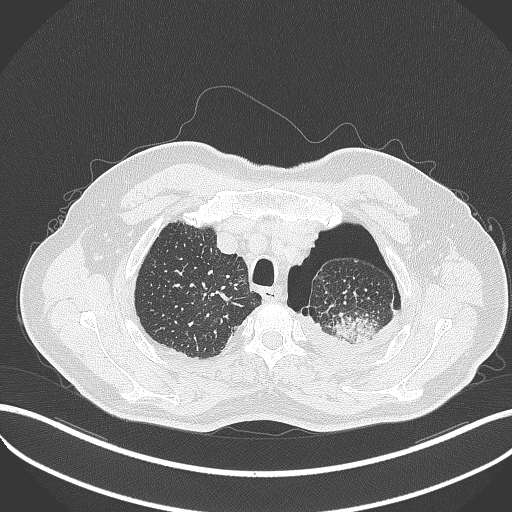
Chest CT, one axial slice; slice 420 of 464 in the series (ordered by position); lung window (W 1500 / L -600 HU); 512 × 512 image matrix. Patient: male, 76 years. From the clinical record (not read from this slice): clinical TNM (as recorded): T3 N0 M1b.
Structures marked on this image (bounding box drawn by a radiologist):
- lung tumour (recorded histology: adenocarcinoma): bounding box (x1, y1, x2, y2) in pixels: (333, 314, 385, 343)